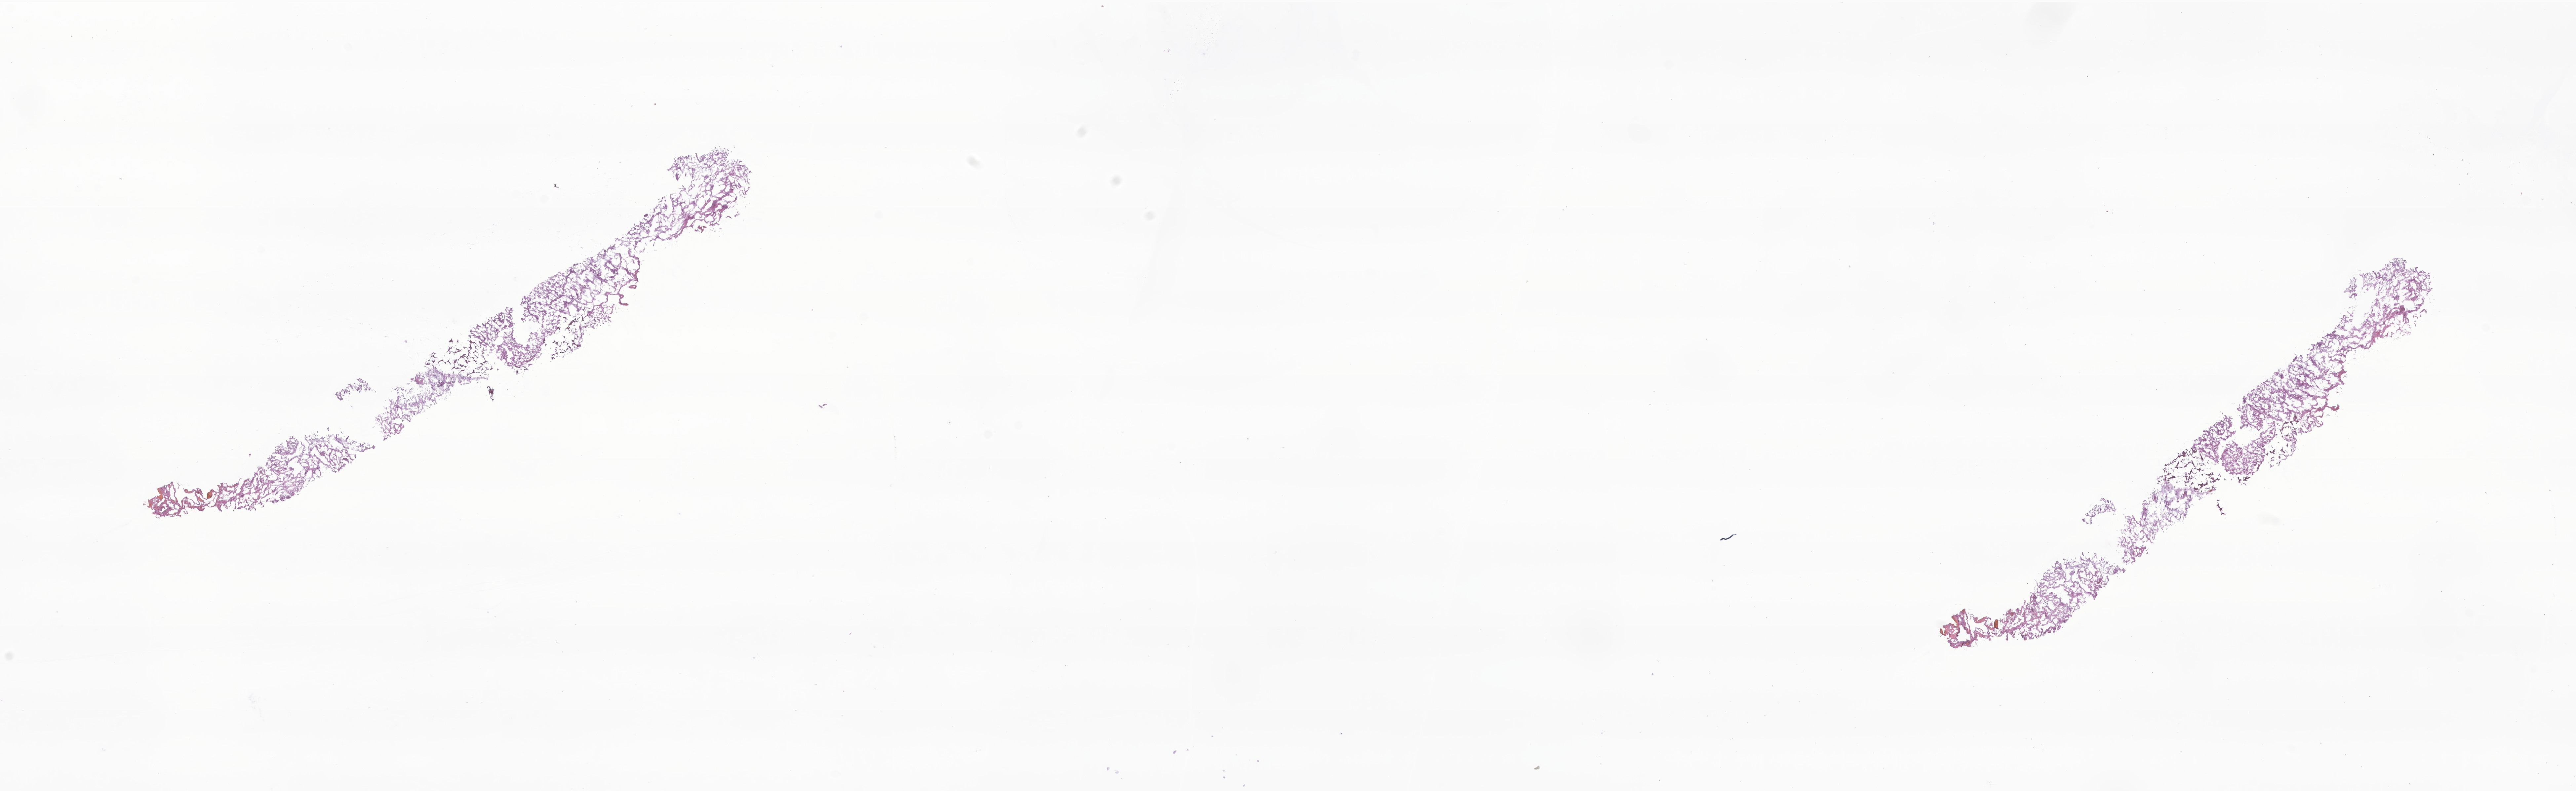
Hematoxylin and eosin (H&E) whole-slide image of tumor tissue from the parietal lobe, a low-resolution overview of the entire scanned area, about 32.9 x 10.1 mm, frozen section (OCT-embedded). Female patient, age 166 months (13 years 10 months).
Diagnosis (ICD-O-3 morphology term): Glioma, malignant.